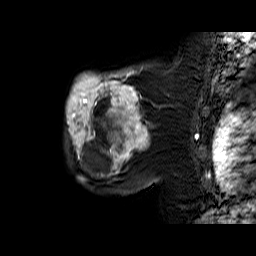
Breast MRI (dynamic contrast-enhanced), one sagittal slice; position 47 of 60 along the scan axis; dynamic contrast-enhanced series, time point 2 of 6 at this slice position (early post-contrast); 1.5 T; TE 6.4 ms, TR 32.9 ms; 256 × 256 image matrix, field of view 200 × 200 mm. Female patient. From the clinical record (not read from this slice): setting: breast cancer imaged before/during neoadjuvant chemotherapy; receptor status: triple-negative.
Structures marked on this image (semi-automatically segmented with operator editing):
- analysis volume of interest (the breast-tissue region the enhancement analysis was run in; not a lesion): box from (x=66, y=65) to (x=159, y=174) px
- tumour enhancement mask (voxels above the 100 % enhancement threshold inside the analysis volume of interest): (x=67, y=65)–(x=148, y=174)